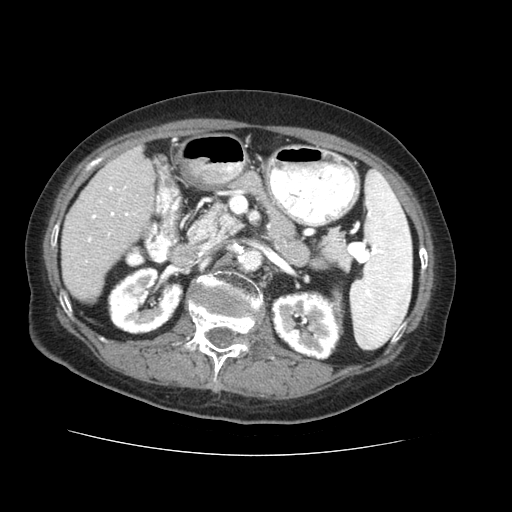
Contrast-enhanced abdominal CT (liver protocol), one axial slice. Position 18 of 73 along the scan axis. Reconstruction kernel STANDARD. Soft-tissue window (W 400 / L 40 HU). 2.5 mm slice thickness. 512 × 512 image matrix, field of view 360 × 360 mm. Case-level facts recorded for this patient, not image findings: diagnosis: hepatocellular carcinoma (patient treated with transarterial chemoembolisation; whether this scan precedes or follows treatment is not stated here); TNM stage (as recorded): Stage-IVB; Child-Pugh class: A.
Annotated regions visible in this slice (semi-automatically segmented with operator editing):
- liver parenchyma outside the tumour (the mass and vessels are separate outlines, so this box may not span the whole liver): bounding box <62,146,154,300> (left, top, right, bottom; pixels)
- liver vessels: <85,177,136,262>